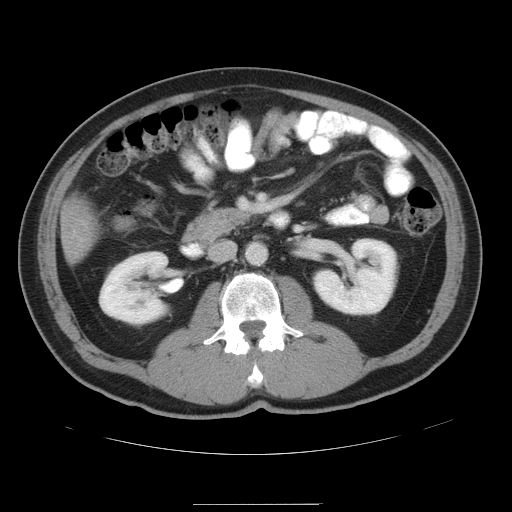
Contrast-enhanced abdominal CT, one axial slice. Position 17 of 47 along the scan axis. Intravenous contrast given. Soft-tissue window (W 400 / L 40 HU). 5 mm slice thickness. 512 × 512 image matrix, field of view 420 × 420 mm. Male patient, age 61 years. Case-level facts recorded for this patient, not image findings: diagnosis: colorectal cancer liver metastases, imaged before liver resection; multiple liver metastases: no.
Structures marked on this image (manually delineated by an expert):
- liver: bounding box <63,202,98,259> (left, top, right, bottom; pixels)
- planned liver remnant (the part of the liver to remain after resection): <75,203,86,211>